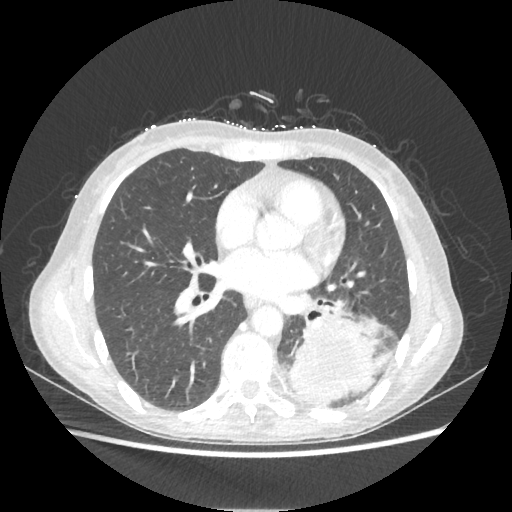
Chest CT, one axial slice; slice 102 of 221 in the series (ordered by position); reconstruction kernel STANDARD; lung window (W 1500 / L -600 HU); 512 × 512 image matrix, field of view 360 × 360 mm. Female patient, age 53 years. From the clinical record (not read from this slice): clinical TNM (as recorded): T3 N0 M0.
Annotated regions visible in this slice (bounding box drawn by a radiologist):
- lung tumour (recorded histology: adenocarcinoma): bounding box [x1, y1, x2, y2] px = [289, 304, 392, 406]